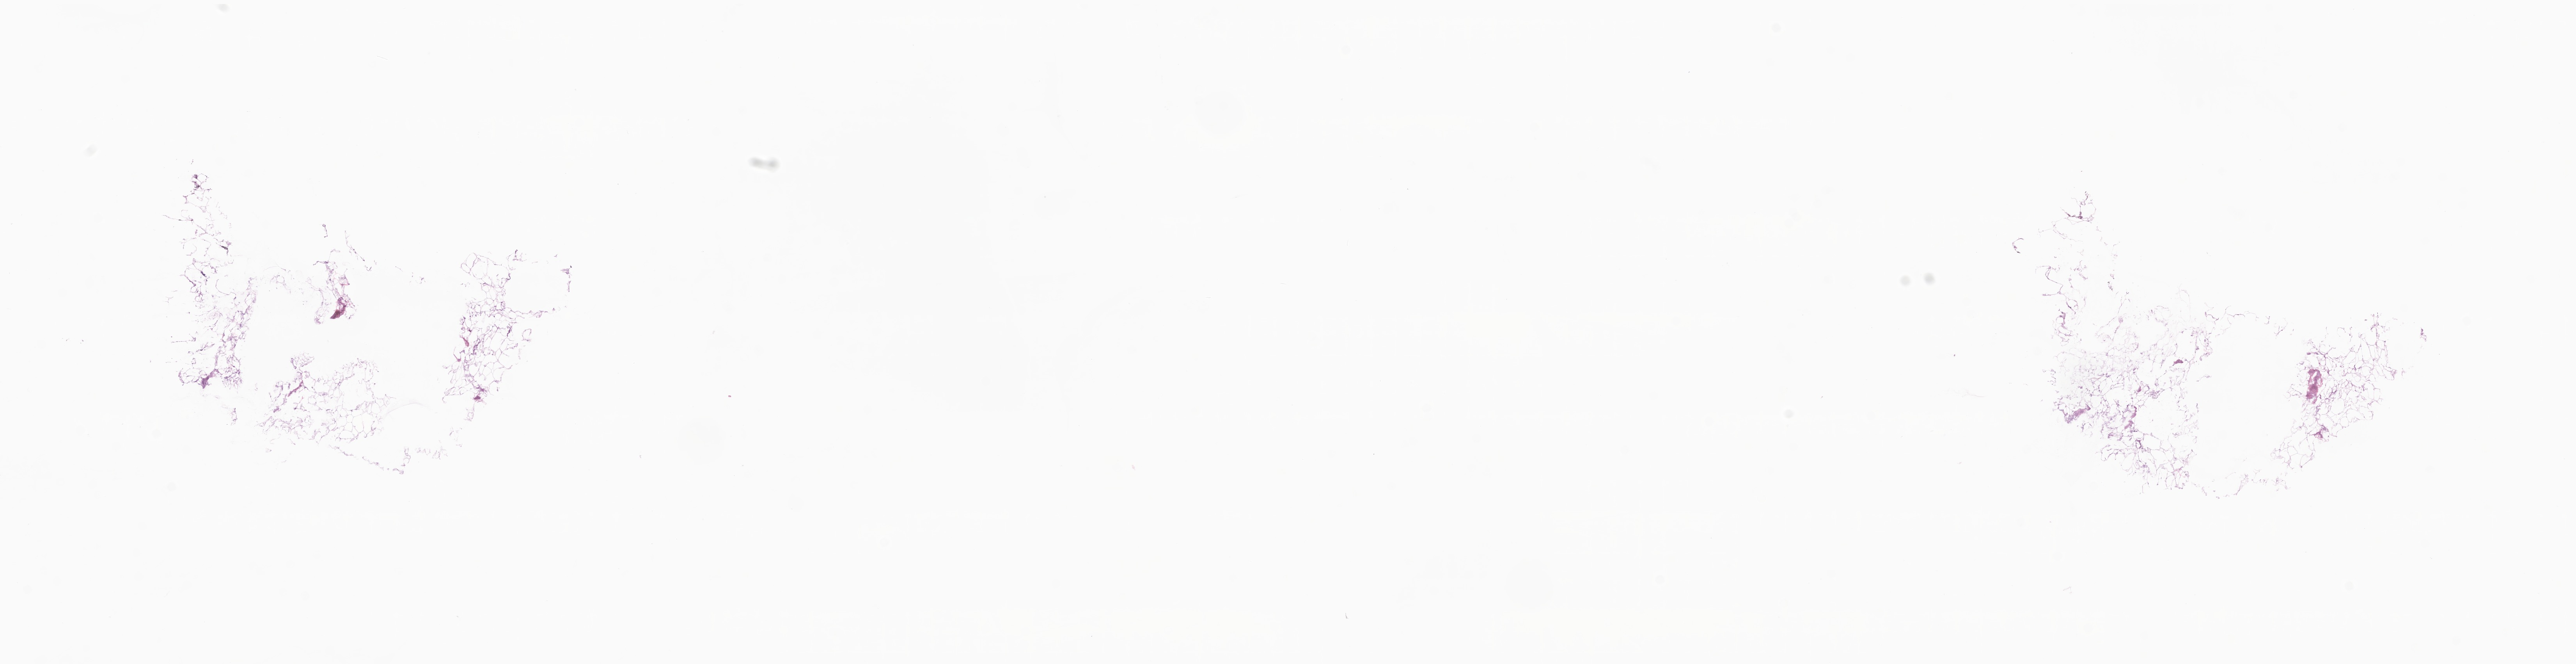
Haematoxylin and eosin whole-slide image, low-resolution overview of the scanned area, about 27.8 x 7.2 mm; cryosection; specimen: primary tumor; site: breast (left). Female patient; age at initial diagnosis 50 years.
Diagnosis: Lobular carcinoma, NOS.